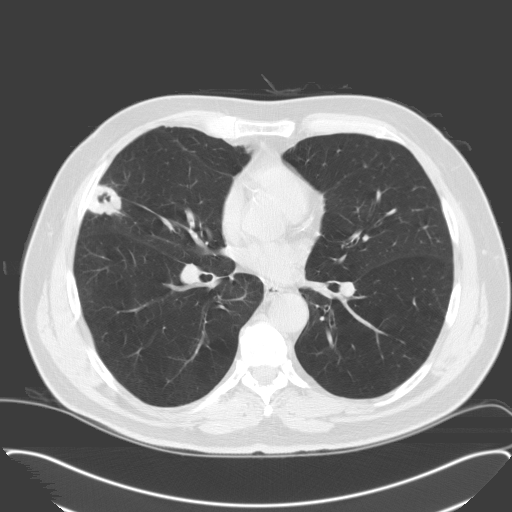
Low-dose screening chest CT, one axial slice; slice 90 of 174 in the series (ordered by position); 120 kVp; lung window (W 1500 / L -600 HU); 512 × 512 image matrix.
Structures marked on this image (expert manual segmentation):
- lesion 1 (tumor, middle lobe of right lung): box from (x=88, y=185) to (x=121, y=215) px